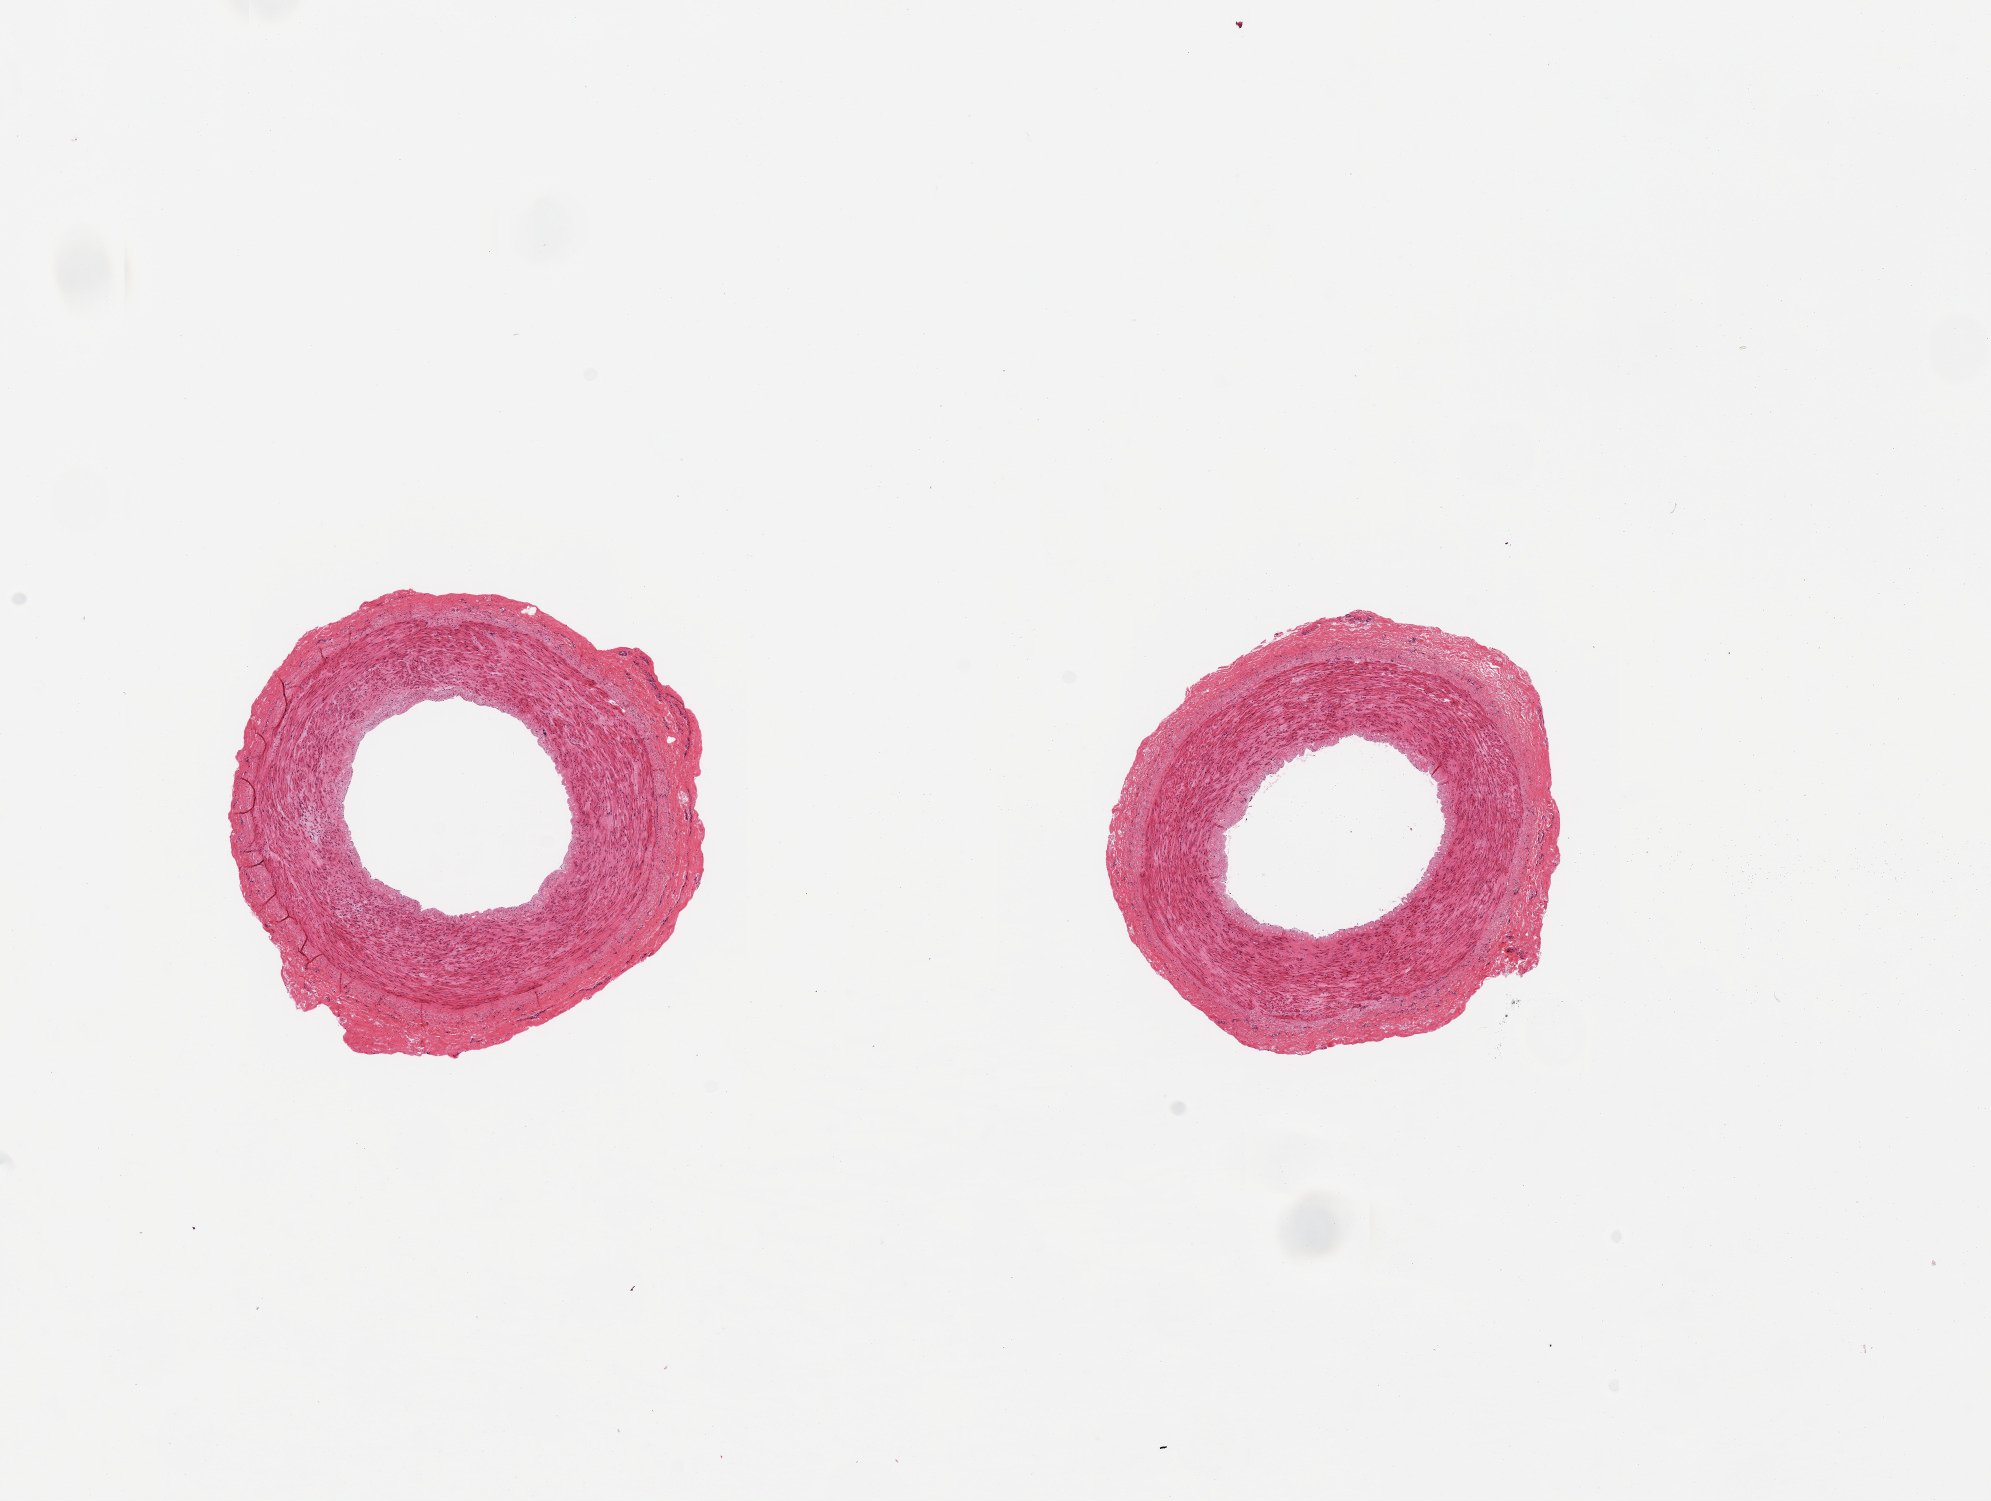
Haematoxylin and eosin whole-slide image, brightfield, low-resolution overview of the scanned area, about 15.8 x 11.9 mm, PAXgene-fixed paraffin-embedded (PFPE) section, sampled site (target tissue): tibial artery, donor tissue sample.
Pathologist's review note for this sample: 2 pieces, well trimmed.